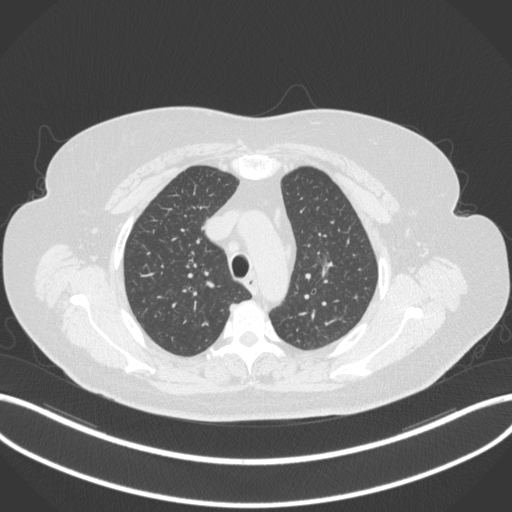
Chest CT, one axial slice. Slice 256 of 310 in the series (ordered by position). Reconstruction kernel B31f. 120 kVp. Lung window (W 1500 / L -600 HU). 1 mm slice thickness. 512 × 512 image matrix, field of view 400 × 400 mm. Female patient, age 70 years. From the clinical record (not read from this slice): clinical TNM (as recorded): T1c N0 M0.
Annotated regions visible in this slice (bounding box drawn by a radiologist):
- lung tumour (recorded histology: adenocarcinoma): bounding box (x1, y1, x2, y2) in pixels: (316, 252, 338, 285)